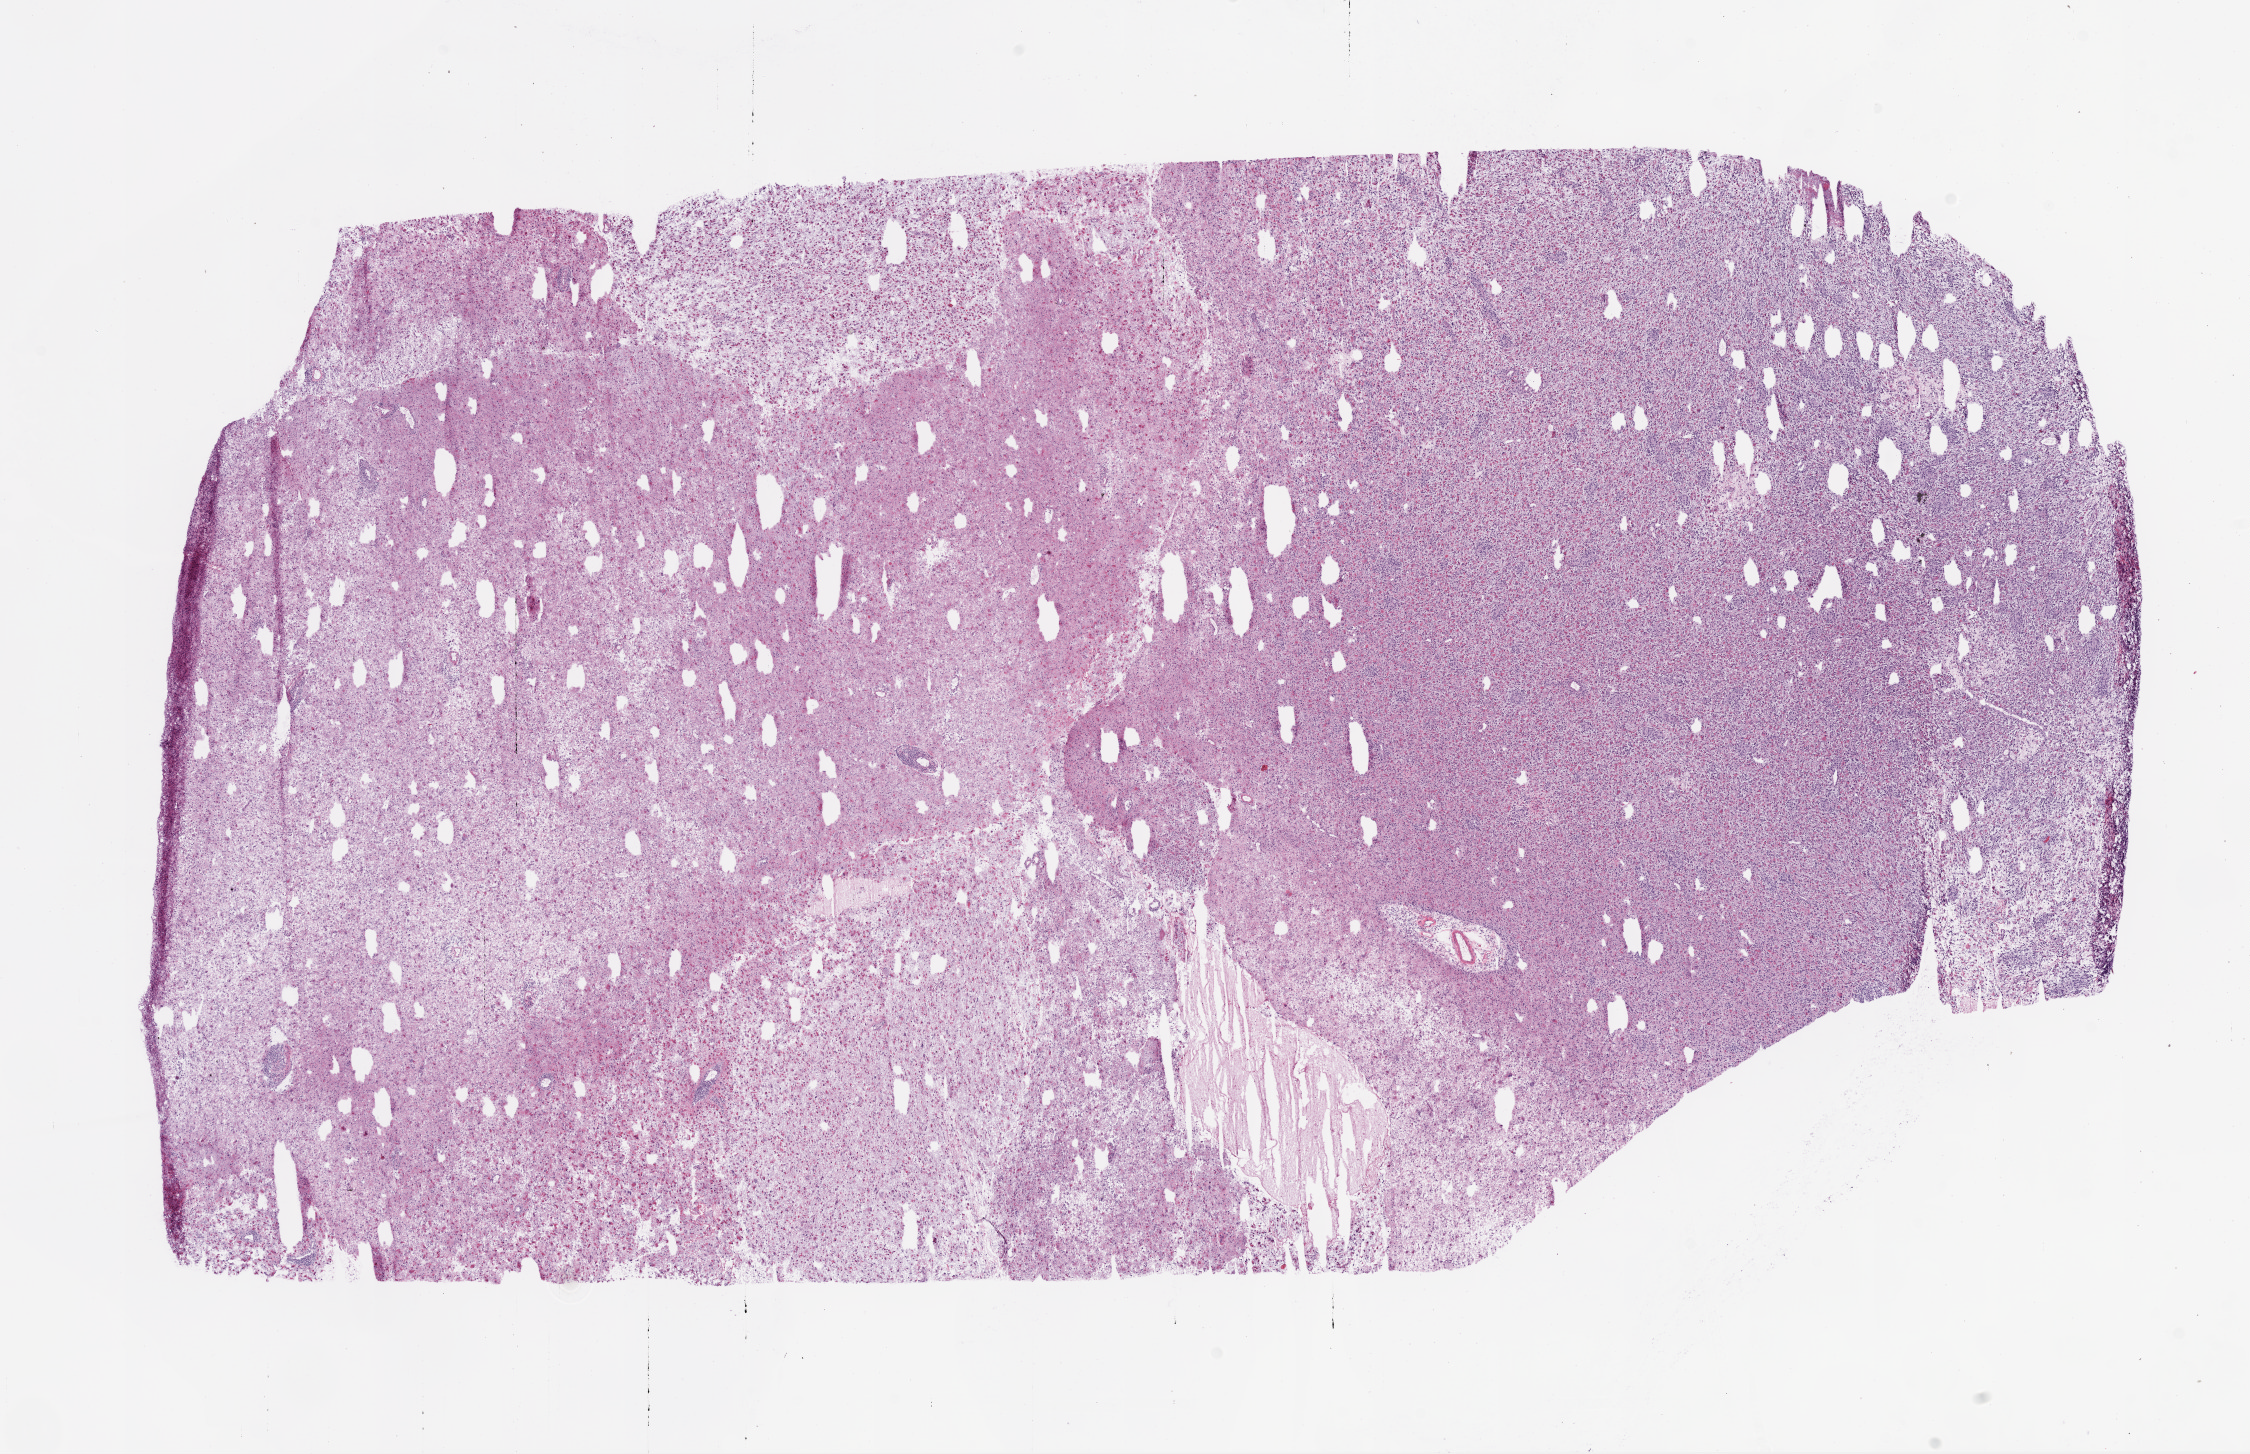
Whole-slide histology image, Hematoxylin and eosin (H&E) stained — low-resolution overview of the scanned area, about 18.1 x 11.7 mm. Frozen section. Brain, primary tumour sample. Male patient; age at initial diagnosis 76 years. Slide review estimates, as recorded: tumour cells 100%, tumour nuclei 80%.
Diagnosis: Glioblastoma.